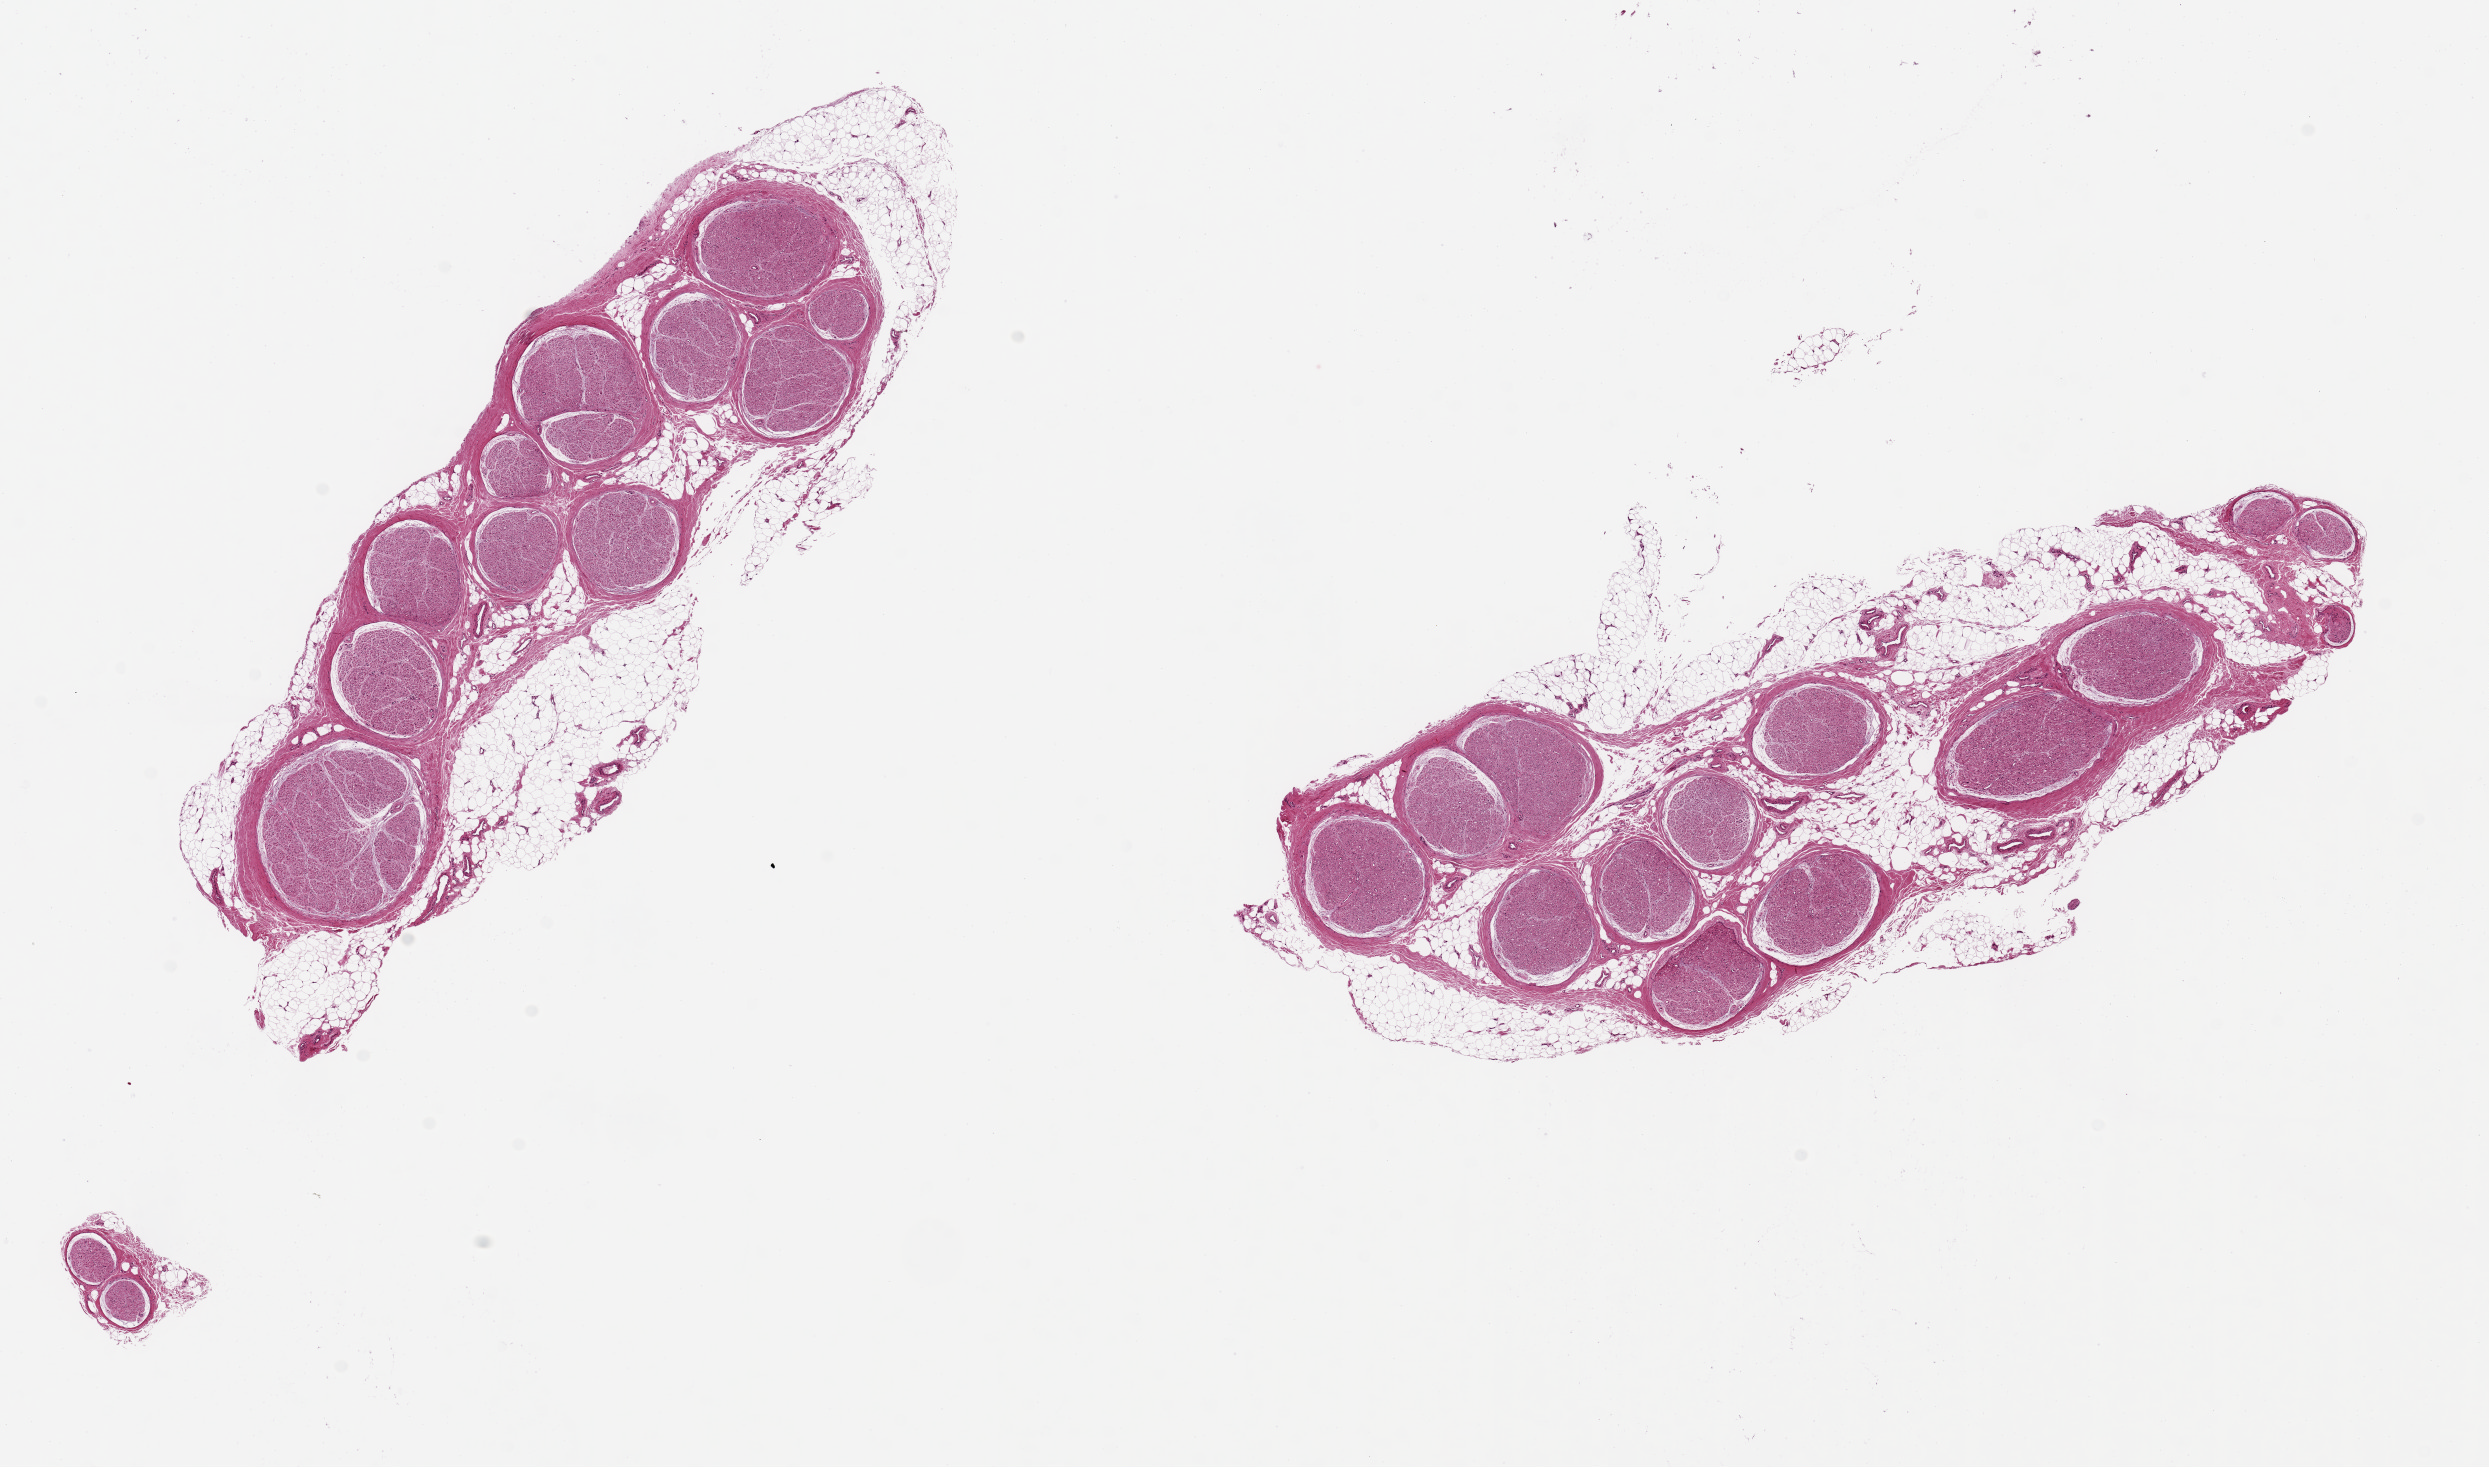
Whole-slide image, H&E stain, whole scanned area (about 19.7 x 11.6 mm) shown as a low-resolution overview; PAXgene-fixed paraffin-embedded (PFPE) section; target tissue: tibial nerve; donor tissue sample. Male donor.
• review note (as recorded): 2 pieces, 9x3 & 9x6mm; 30% peripheral and internal adipose